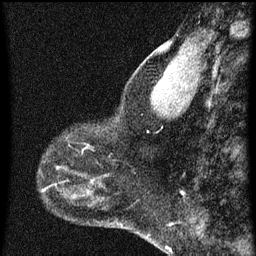
Breast MRI (dynamic contrast-enhanced), one sagittal slice; slice 20 of 60 in the series (ordered by position); dynamic contrast-enhanced series, image 2 of 3 at this slice position (ordered by acquisition); 1.5 T; TE 4.2 ms, TR 8 ms; 256 × 256 image matrix. Female patient, age 44 years.
Structures marked on this image (semi-automatic segmentation, software-assisted and operator-edited):
- analysis volume of interest (the breast-tissue region the enhancement analysis was run in; not a lesion): box from (x=49, y=128) to (x=95, y=169) px
- tumour enhancement mask (voxels above the 70 % enhancement threshold inside the analysis volume of interest): (x=68, y=144)–(x=89, y=149)